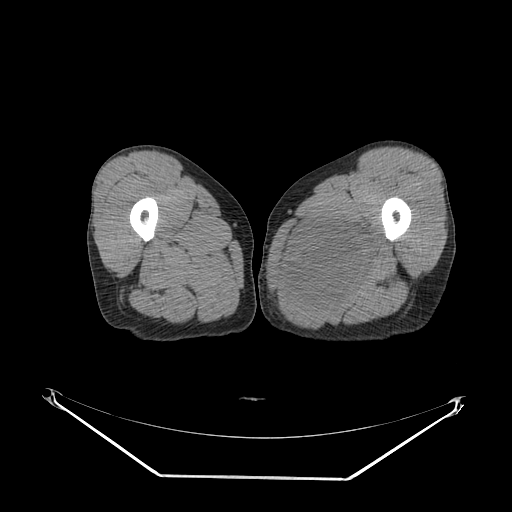
CT of an extremity soft-tissue mass (from a PET/CT study), one axial slice. Position 24 of 267 along the scan axis. Reconstruction kernel SOFT. Soft-tissue window (W 400 / L 40 HU). 512 × 512 image matrix. Male patient. Case-level facts recorded for this patient, not image findings: histological type: pleiomorphic liposarcoma; grade: high; site of the primary tumour: left thigh.
Structures marked on this image (expert contour drawn on MRI and transferred to this co-registered scan by the dataset authors):
- gross tumour volume including surrounding oedema: bounding box (x1, y1, x2, y2) in pixels: (288, 215, 387, 309)
- gross tumour volume (mass): (292, 219, 371, 302)